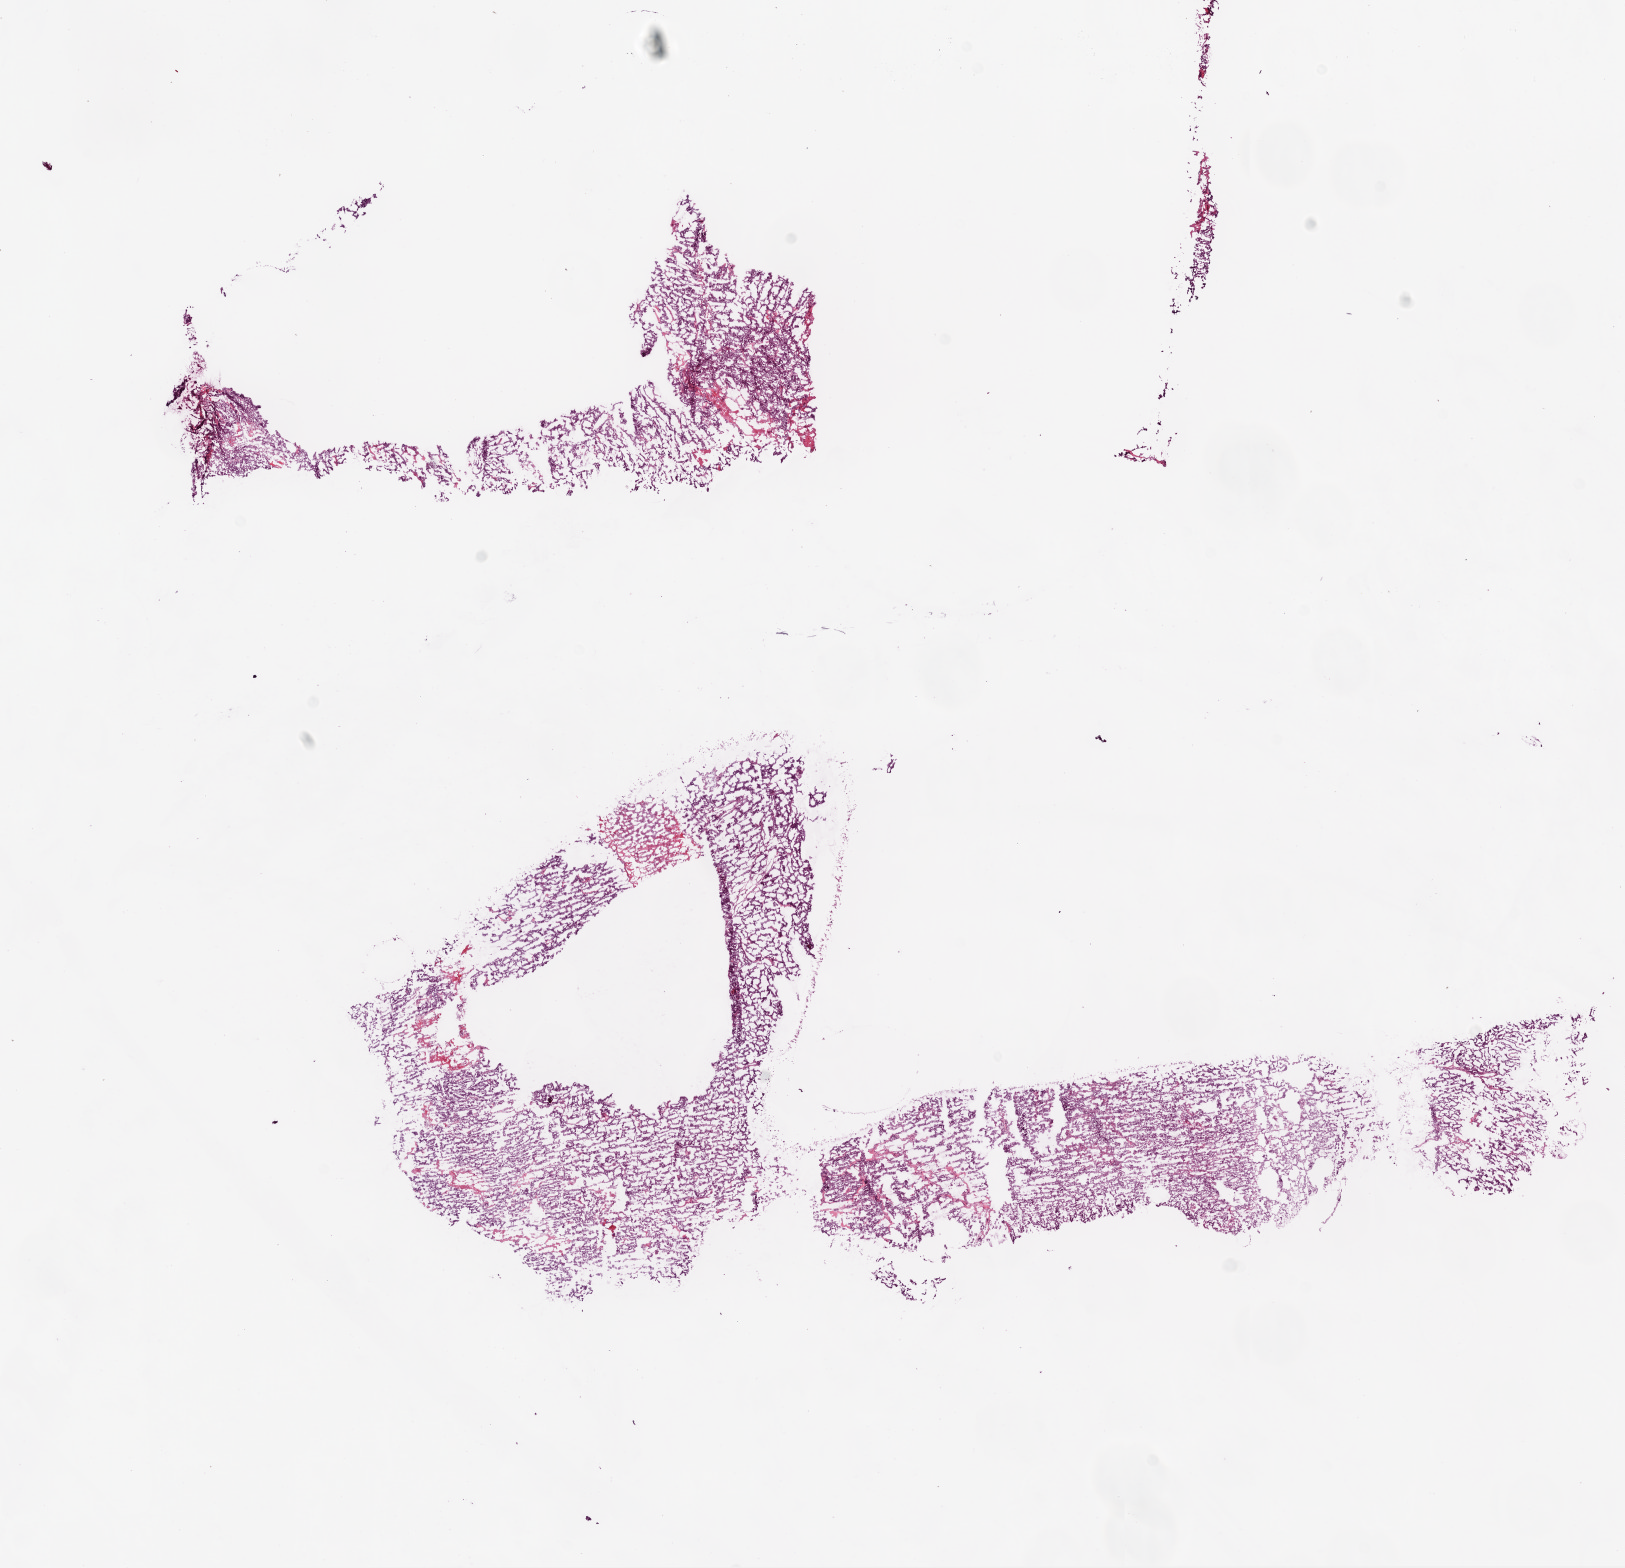
Whole-slide histology image, H&E, a low-resolution overview of the entire scanned area, about 13.0 x 12.6 mm. Frozen section from the bottom of the tissue portion. Sample: primary tumour, ovary. Patient: female, age at initial diagnosis 69 years. Histologic grade: G2 (moderately differentiated). Composition of this section per pathologist review: tumour cells 95%, tumour nuclei 99%, normal cells 0%, stromal cells 5%, necrosis 0%.
FIGO stage: IIIC. Diagnosis: Serous cystadenocarcinoma, NOS. Laterality: bilateral.